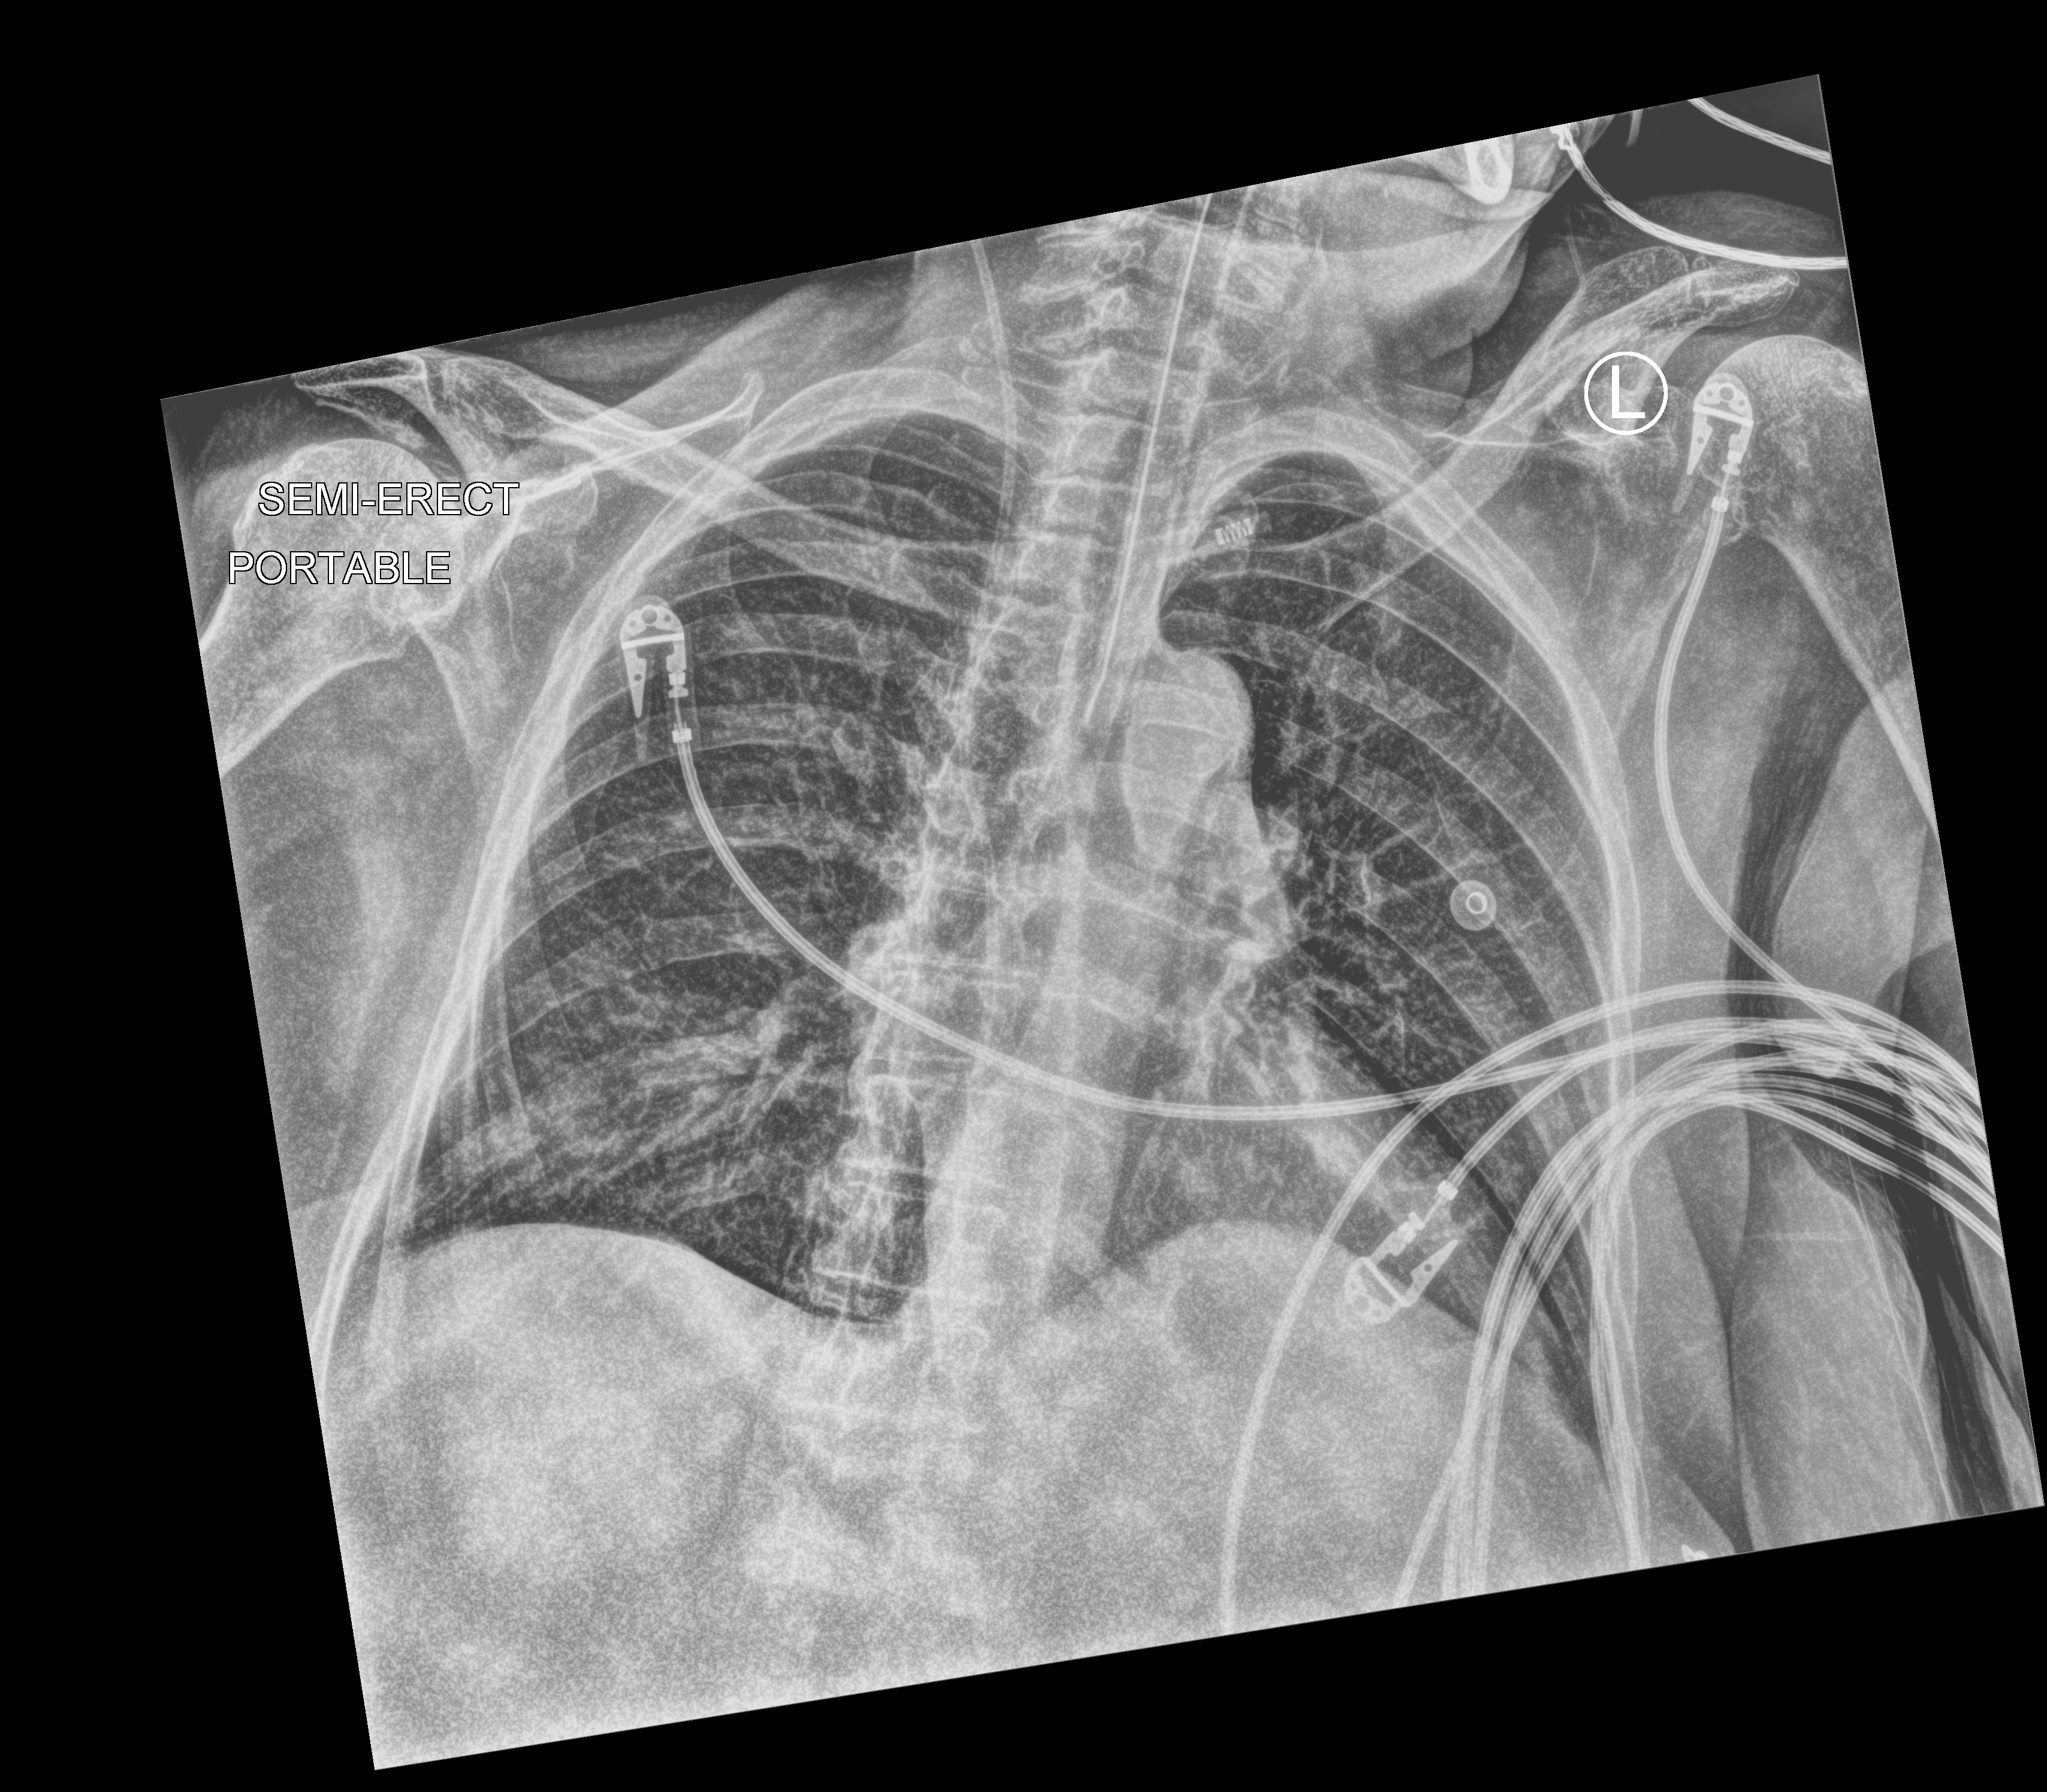
Chest X-ray (portable), anteroposterior (AP) projection. Patient hospitalised with COVID-19; female, aged 75–90 years.
From the hospital-stay record, not from the radiograph (when in the stay this image was taken is not recorded): mechanically ventilated during this hospital stay: yes; admitted to intensive care during this hospital stay: yes.